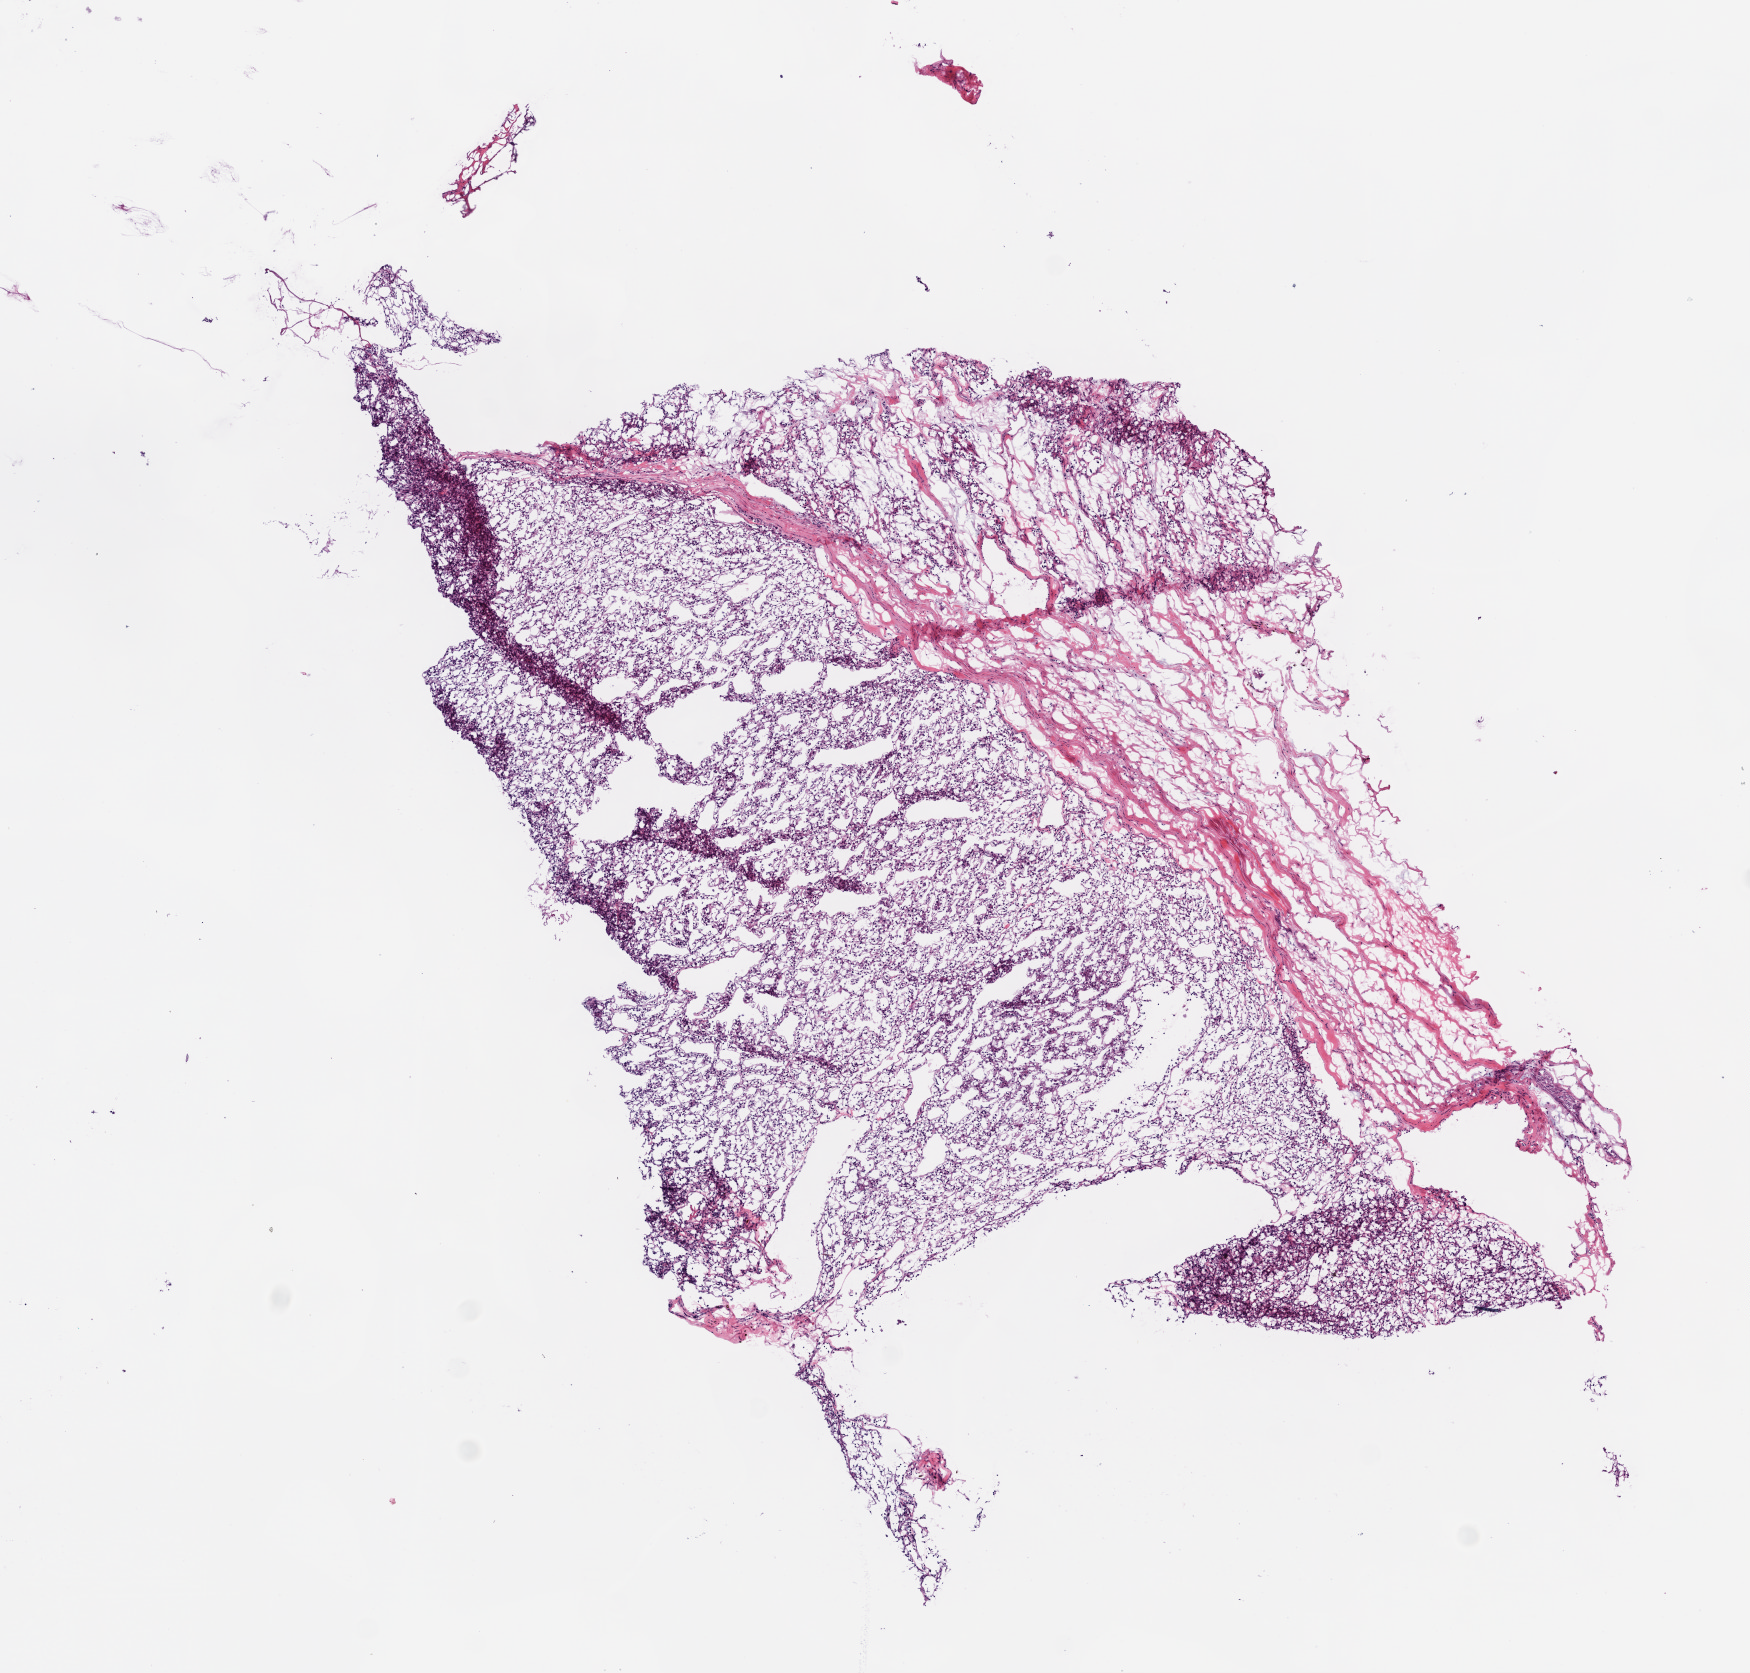
H&E whole-slide image, low-resolution overview of the scanned area, about 7.0 x 6.7 mm; frozen section from the bottom of the tissue portion; sample: primary tumour, kidney. Male, age 84 years at initial diagnosis. Histologic grade: G3 (poorly differentiated). Slide review estimates, as recorded: tumour cells 65%, tumour nuclei 70%, normal cells 0%, stromal cells 35%, necrosis 0%.
Pathologic diagnosis: Clear cell adenocarcinoma, NOS. TNM: T1b NX M0. Laterality: right. AJCC pathologic stage: I.